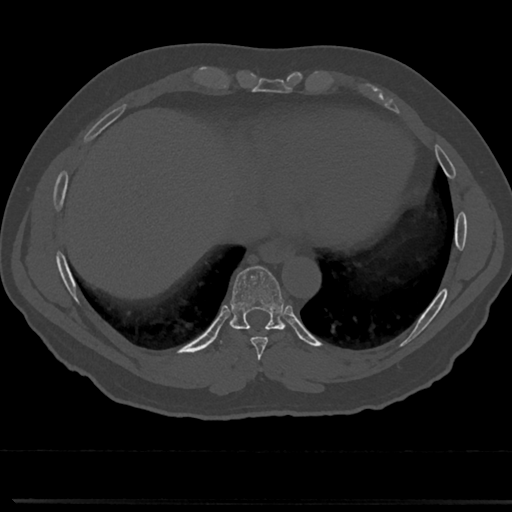
CT including the spine, one axial slice; bone window (W 1800 / L 400 HU); 0.5 mm slice thickness; 512 × 512 image matrix, field of view 355 × 355 mm. Patient: male, 61 years. Case-level facts recorded for this patient, not image findings: primary cancer: prostate.
Structures marked on this image (semi-automatic segmentation, software-assisted and operator-edited):
- T7 vertebra: bounding box <258,357,266,376> (left, top, right, bottom; pixels)
- T8 vertebra: <213,269,309,357>